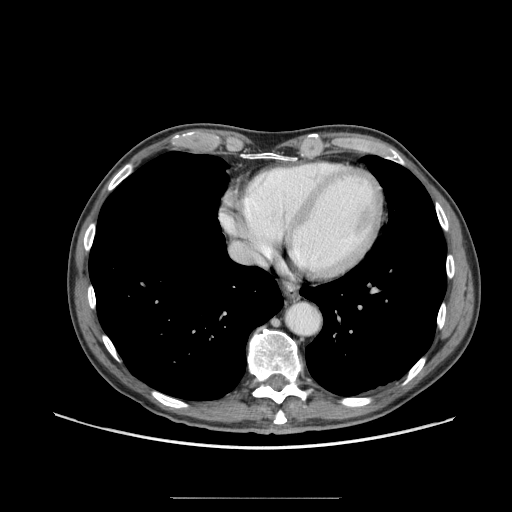
Contrast-enhanced abdominal CT (liver protocol), one axial slice. Reconstruction kernel STANDARD. 140 kVp. Soft-tissue window (W 400 / L 40 HU). 2.5 mm slice thickness. 512 × 512 image matrix, field of view 400 × 400 mm. From the clinical record (not read from this slice): diagnosis: hepatocellular carcinoma (patient treated with transarterial chemoembolisation; whether this scan precedes or follows treatment is not stated here); TNM stage (as recorded): Stage-I; Child-Pugh class: A; tumour differentiation: well differentiated; tumour nodularity: uninodular.
Outlined on this slice (semi-automatically segmented with operator editing):
- abdominal aorta: bounding box (x1, y1, x2, y2) in pixels: (286, 303, 319, 335)